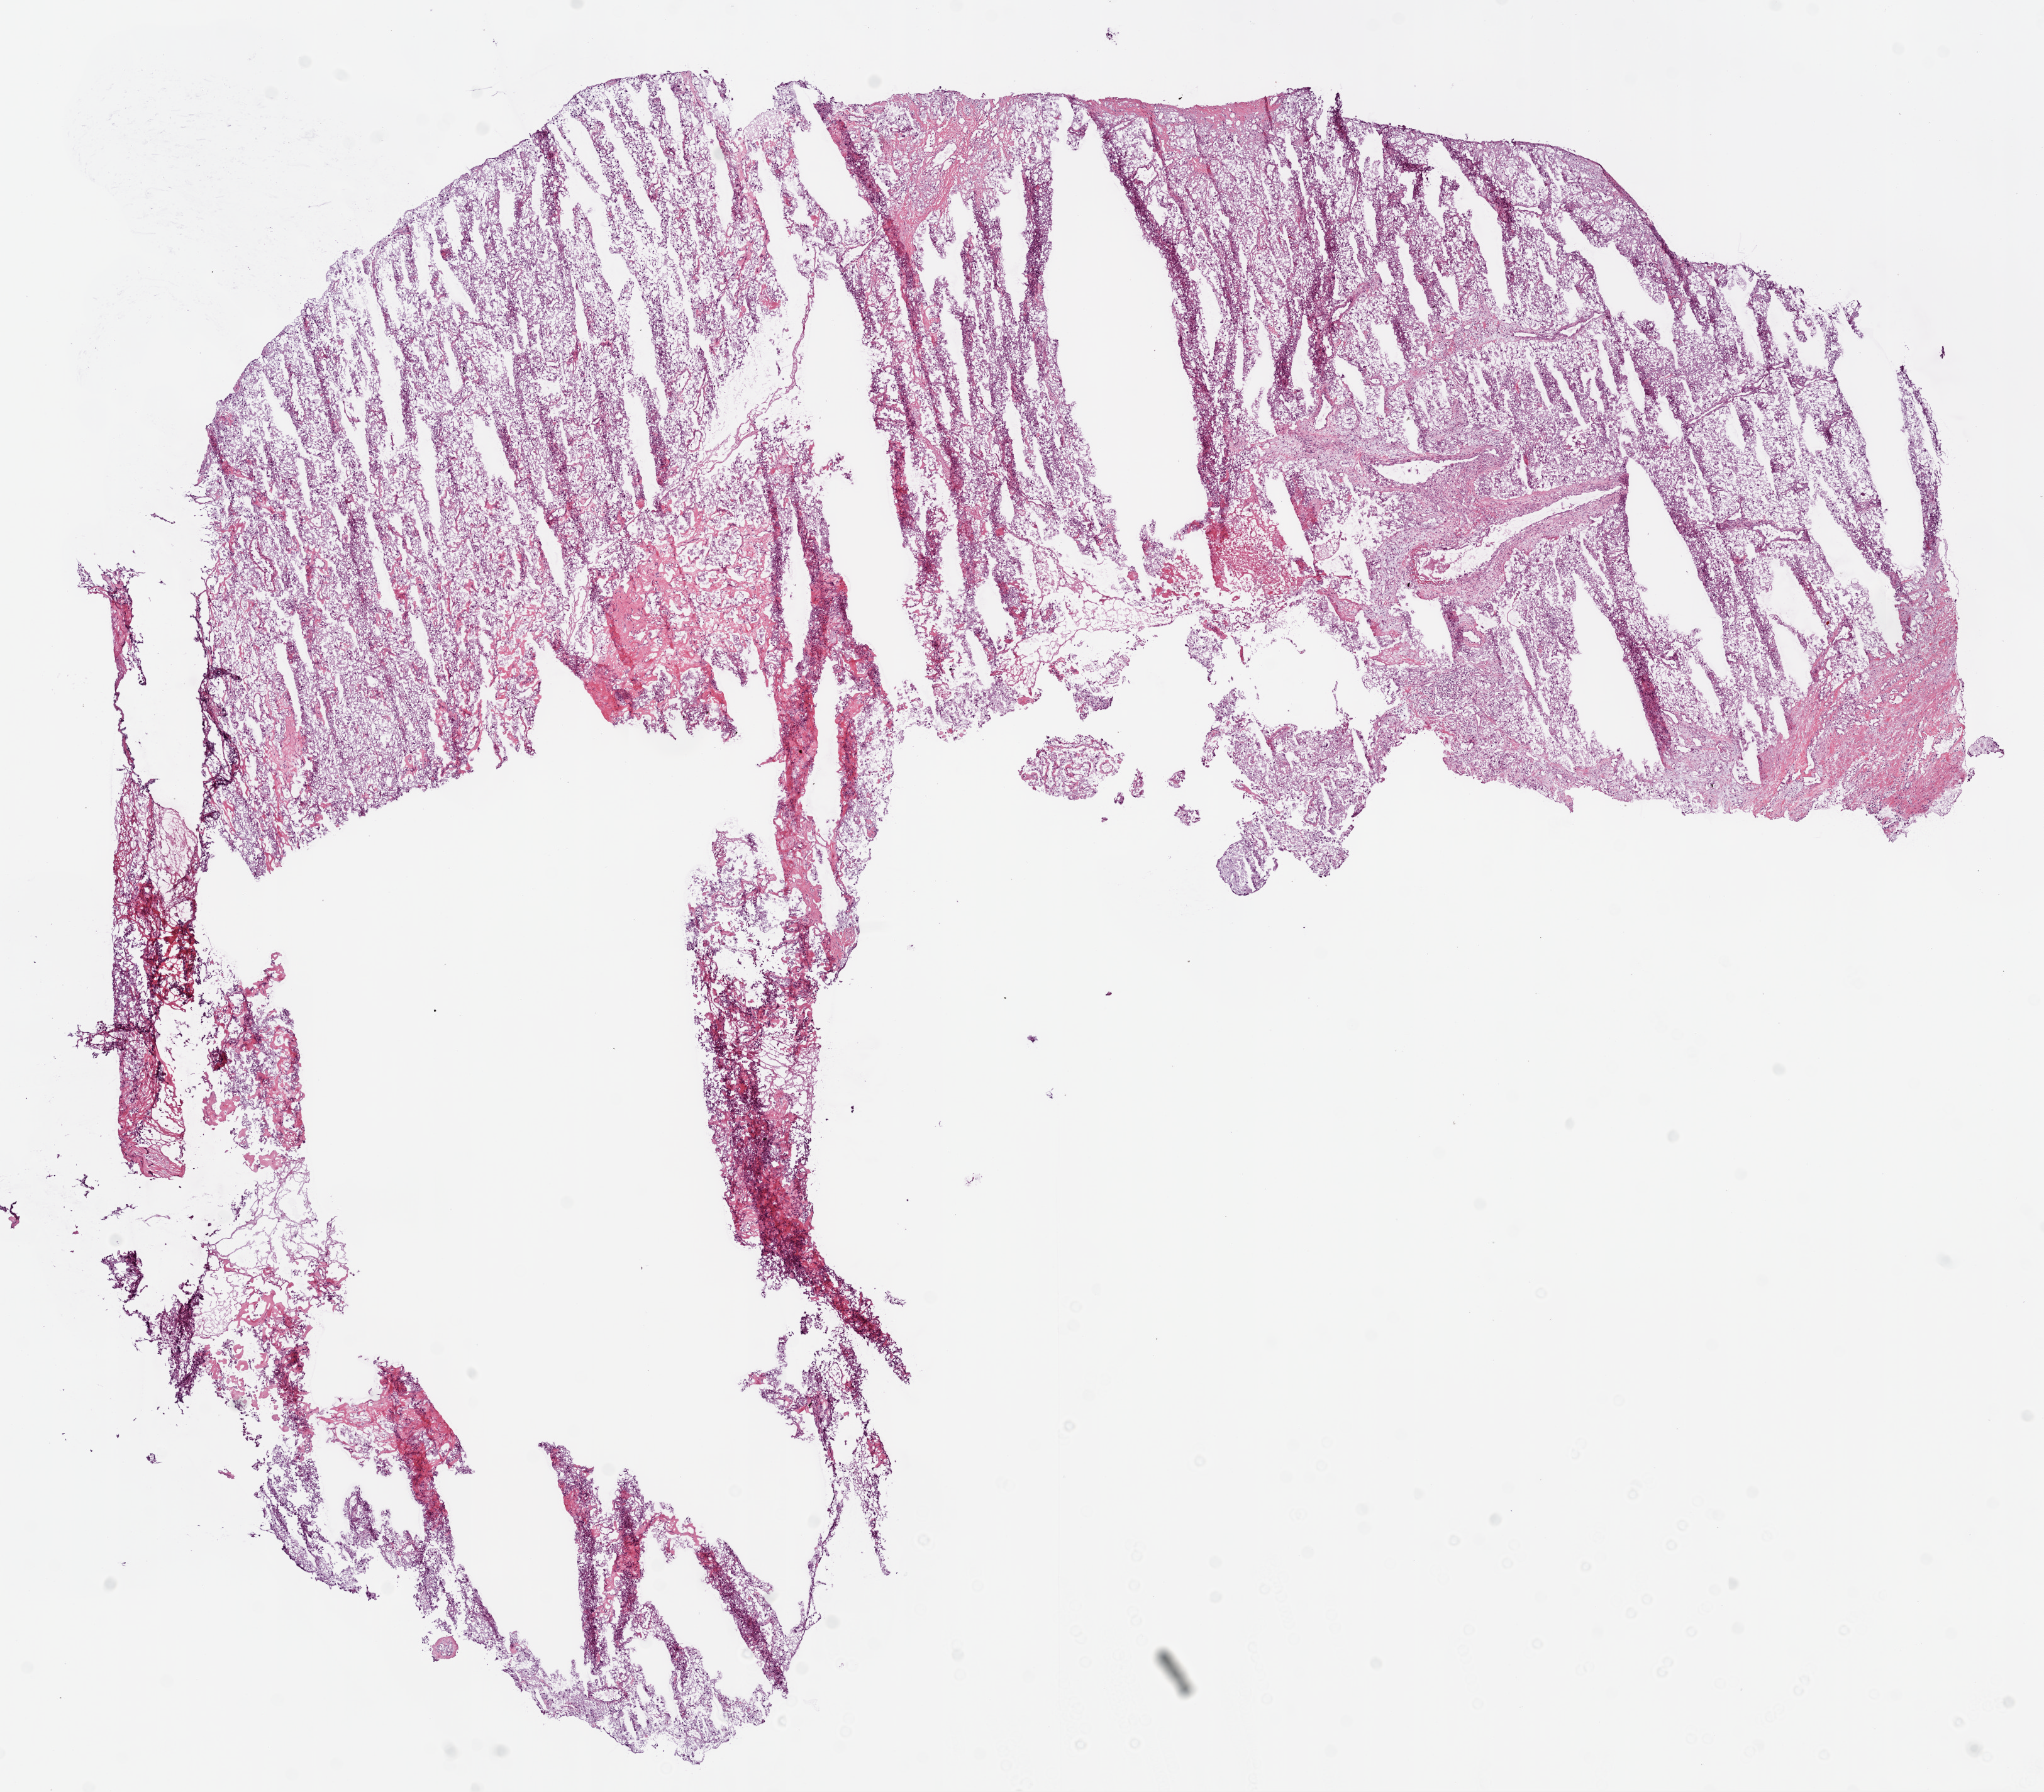
Digitized H&E tissue section (whole slide) — a low-resolution overview of the entire scanned area, about 13.0 x 11.4 mm, frozen section from the bottom of the tissue portion, primary tumour sample from the kidney. Male patient; age at initial diagnosis 72 years. Histologic grade: G4 (undifferentiated). Slide review estimates, as recorded: tumour cells 85%, tumour nuclei 85%, normal cells 0%, stromal cells 10%, necrosis 5%.
- TNM: T3a N0 M0
- histologic diagnosis: Clear cell adenocarcinoma, NOS
- AJCC pathologic stage: III